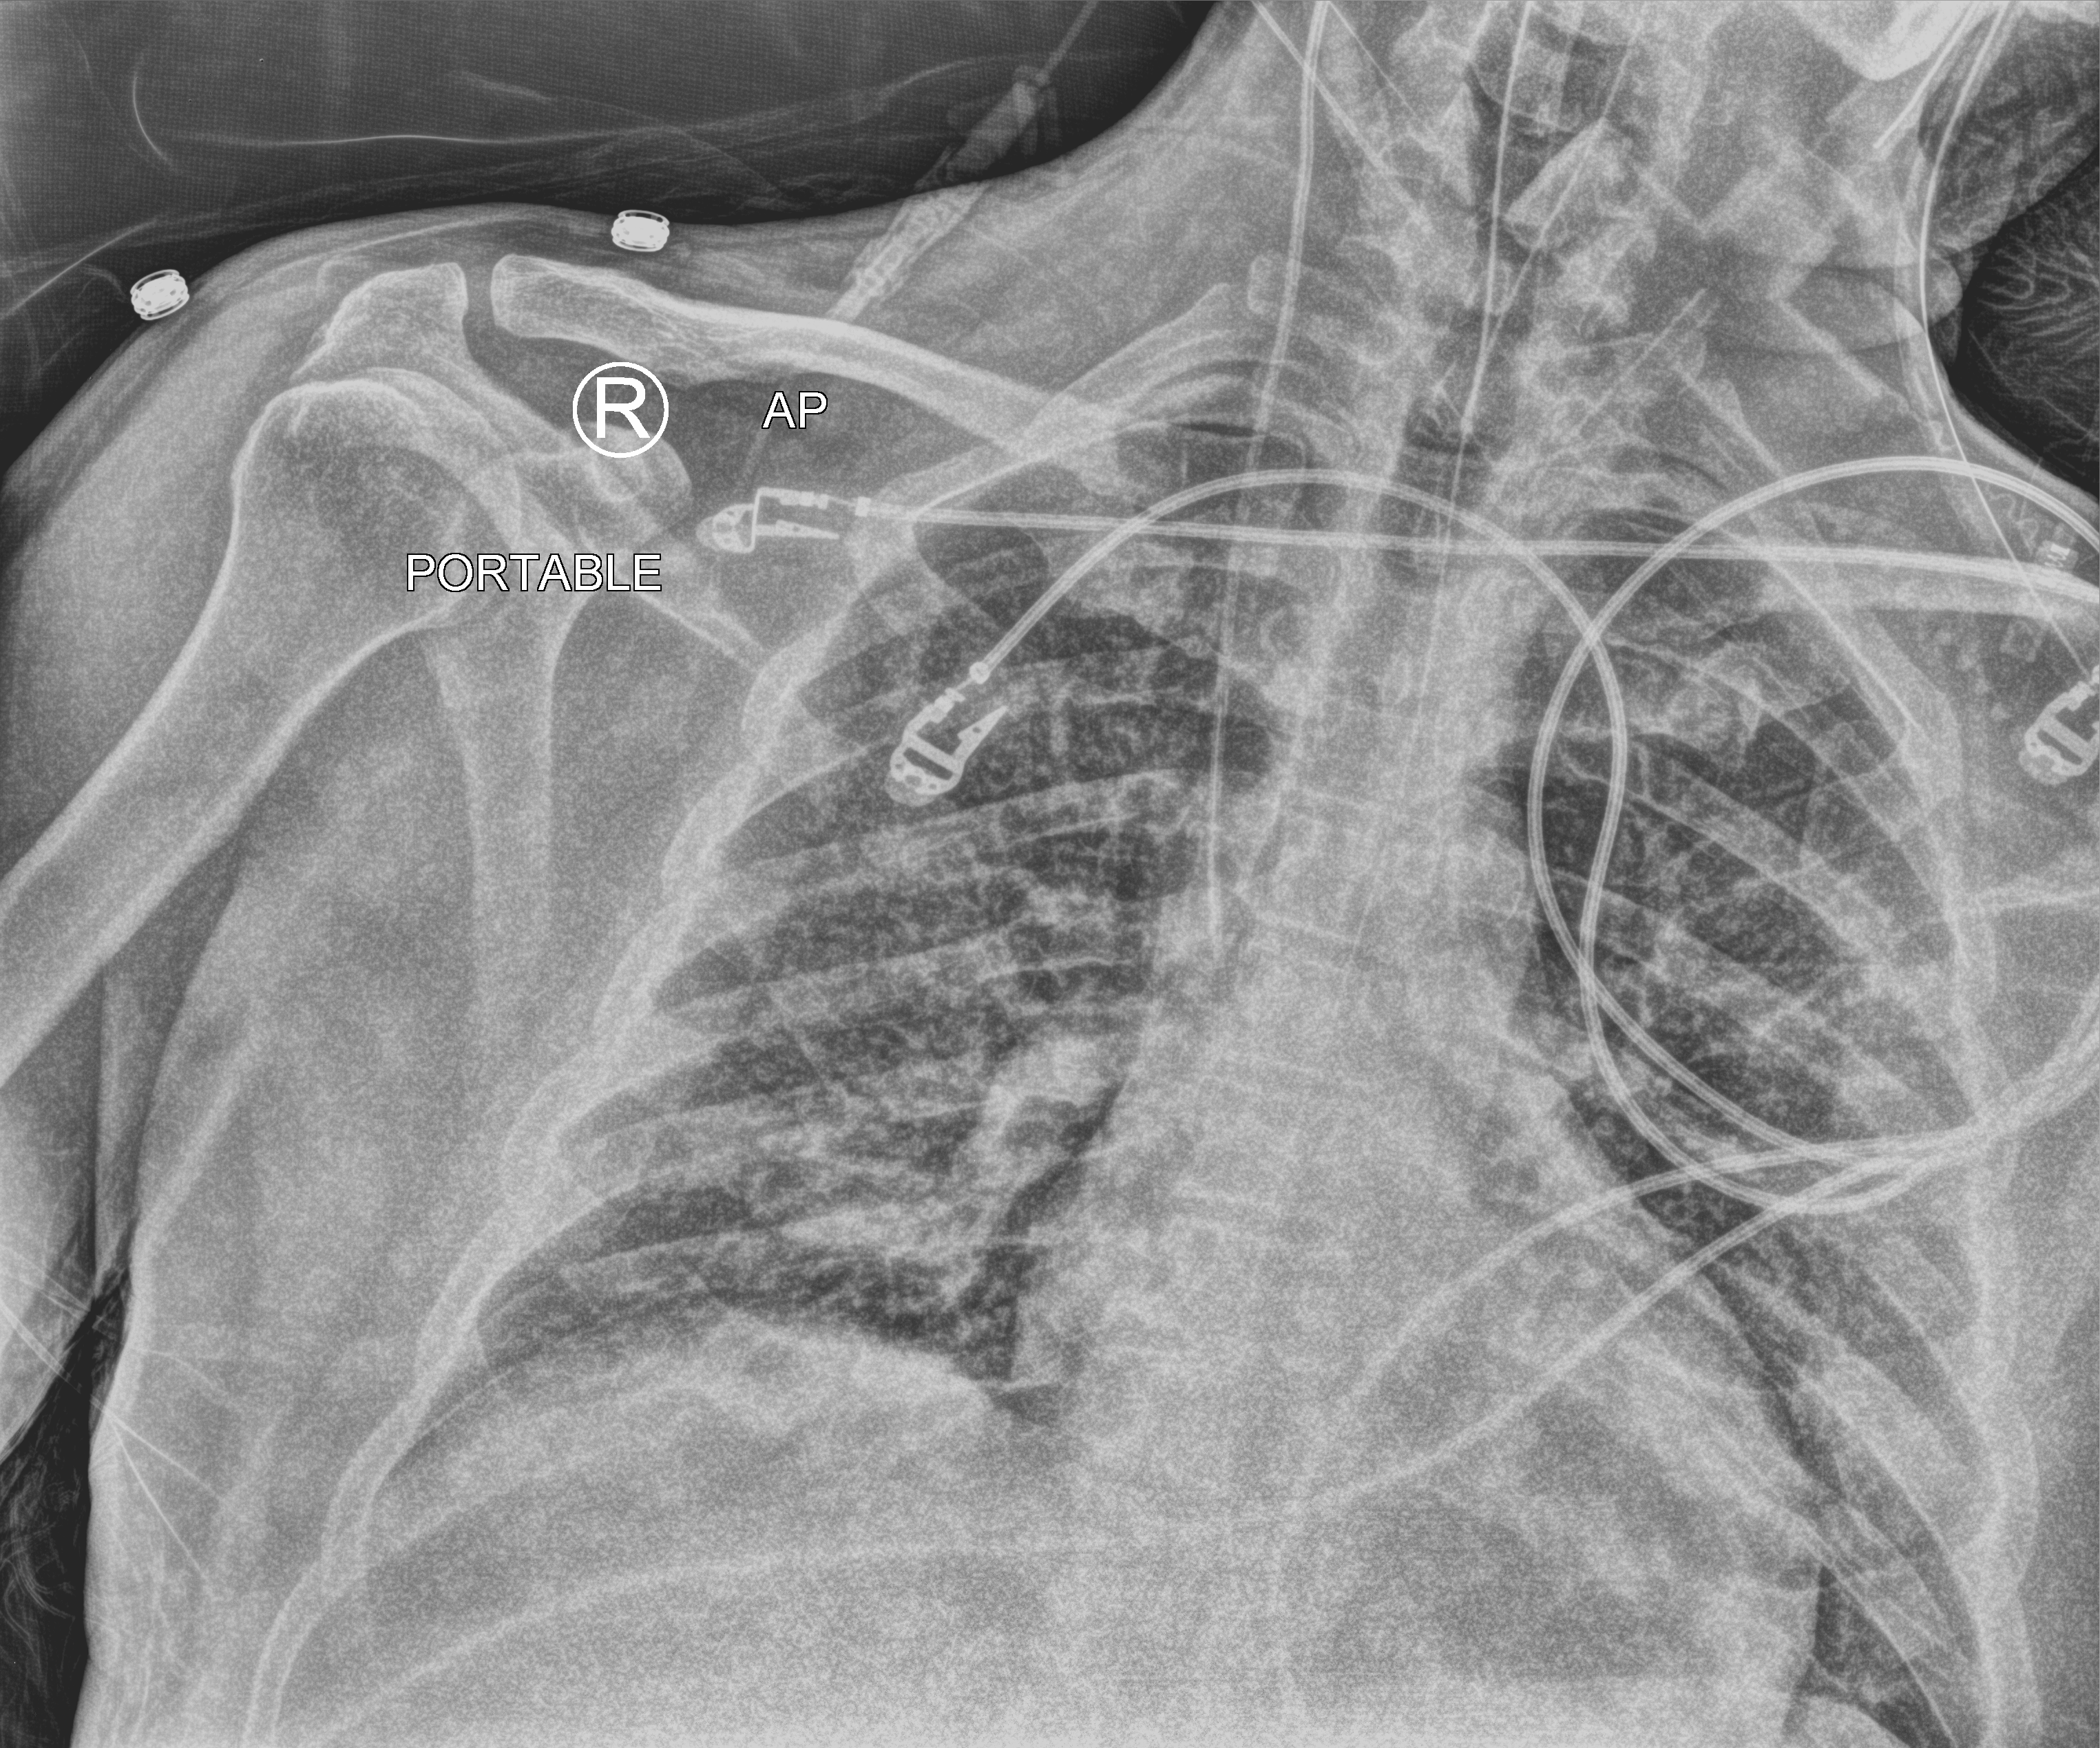
Chest X-ray (portable). Male patient hospitalised with COVID-19, age 18–59 years.
Admission-level facts for this patient (not findings on this image; timing relative to this image not recorded):
- admitted to intensive care during this hospital stay: no
- mechanically ventilated during this hospital stay: yes